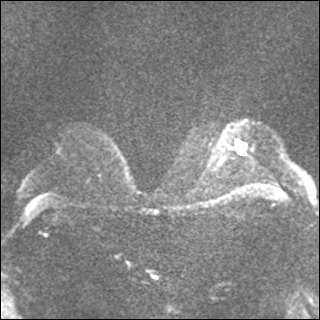
Breast MRI, one axial slice. Position 22 of 35 along the scan axis. Diffusion-weighted series; image 2 of 4 stored at this slice position (different b-values; order by instance number). 1.5 T. 4 mm slice thickness. 320 × 320 image matrix. Female patient.
Annotated regions visible in this slice (manually delineated by an expert):
- tumour on diffusion-weighted imaging: bounding box (x1, y1, x2, y2) in pixels: (237, 141, 244, 153)